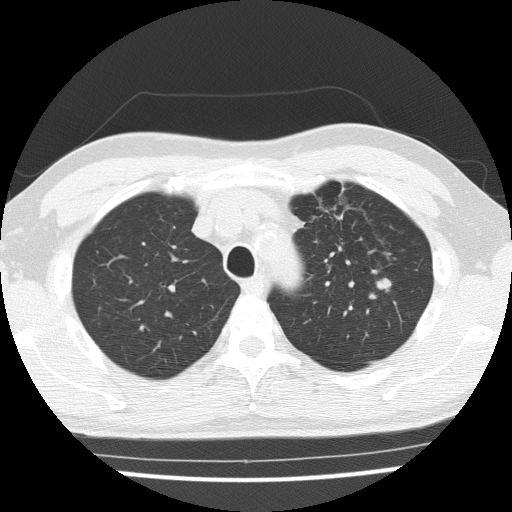
Axial slice from a low-dose chest CT screening exam, third annual screen, lung window (W 1500 / L -600 HU), 2 mm slice thickness, lung (sharp) reconstruction kernel (FC51), slice 39 of 154 in the series, 512 × 512 image matrix, field of view 330 × 330 mm. Male participant, aged 65 years at enrolment. Current smoker at enrolment.
Expert reader's lesion annotation, bounding box (x1, y1, x2, y2) in pixels: (354, 268, 406, 312). The exam's reader record, not a measurement of the box and not confirmed to be the same lesion: non-calcified nodule or mass ≥4 mm, left upper lobe, 16 × 15 mm, poorly defined margins, soft tissue attenuation, pre-existing on the prior screen: yes; interval growth: yes. Lung cancer was diagnosed 42 days after this screen: squamous cell carcinoma, NOS, left upper lobe, moderately differentiated (G2), stage IA (AJCC 6th edition), 25 mm at pathology.